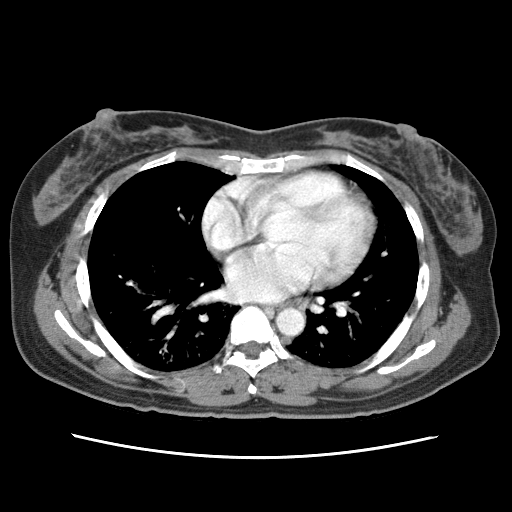
Contrast-enhanced abdominal CT (liver protocol), one axial slice. Position 76 of 79 along the scan axis. Reconstruction kernel STANDARD. Soft-tissue window (W 400 / L 40 HU). 2.5 mm slice thickness. 512 × 512 image matrix, field of view 340 × 340 mm. Case-level facts recorded for this patient, not image findings: diagnosis: hepatocellular carcinoma (patient treated with transarterial chemoembolisation; whether this scan precedes or follows treatment is not stated here); TNM stage (as recorded): Stage-I; Child-Pugh class: A; tumour differentiation: moderately differentiated; tumour nodularity: uninodular.
Structures marked on this image (semi-automatic segmentation, software-assisted and operator-edited):
- abdominal aorta: bounding box [x1, y1, x2, y2] px = [276, 308, 305, 336]